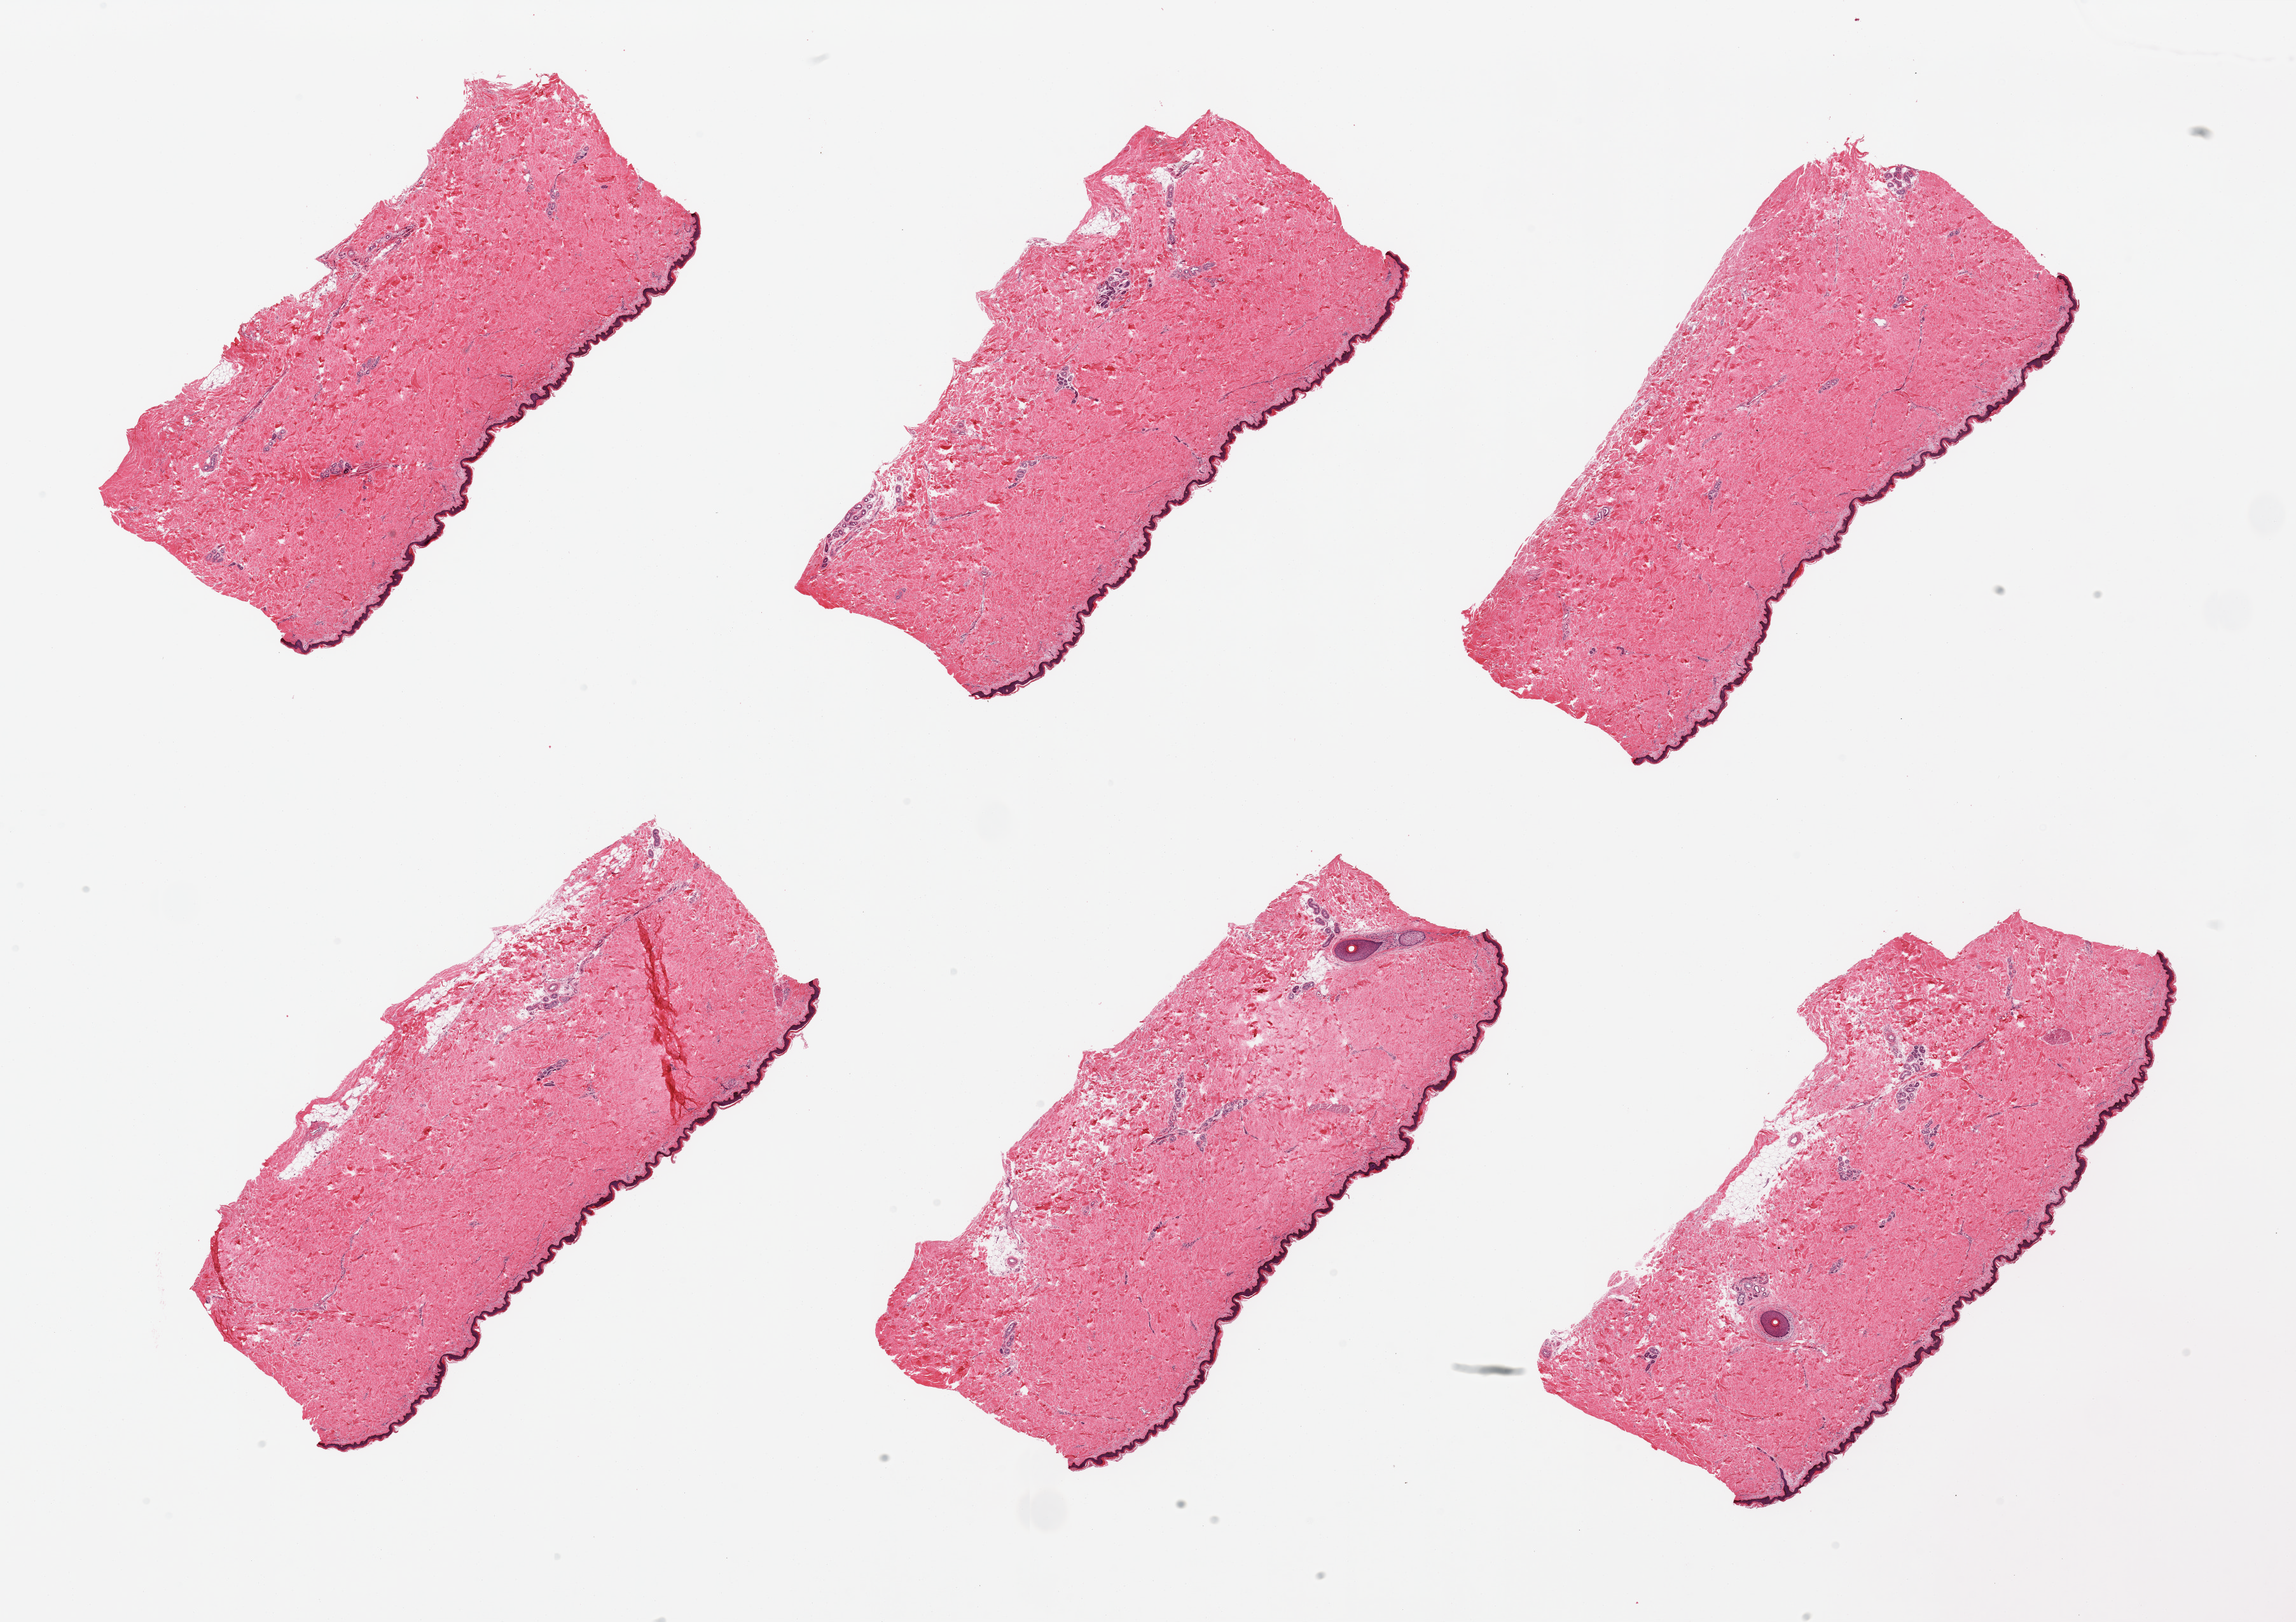
Haematoxylin and eosin whole-slide image, brightfield — whole scanned area (about 28.5 x 20.2 mm) shown as a low-resolution overview; PAXgene-fixed paraffin-embedded (PFPE) section; sampled site (target tissue): skin of suprapubic region; tissue donor sample.
Reviewer comment on this tissue sample: 6 pieces, minimal dermal fat; squamous epithelium is ~40-50 microns.